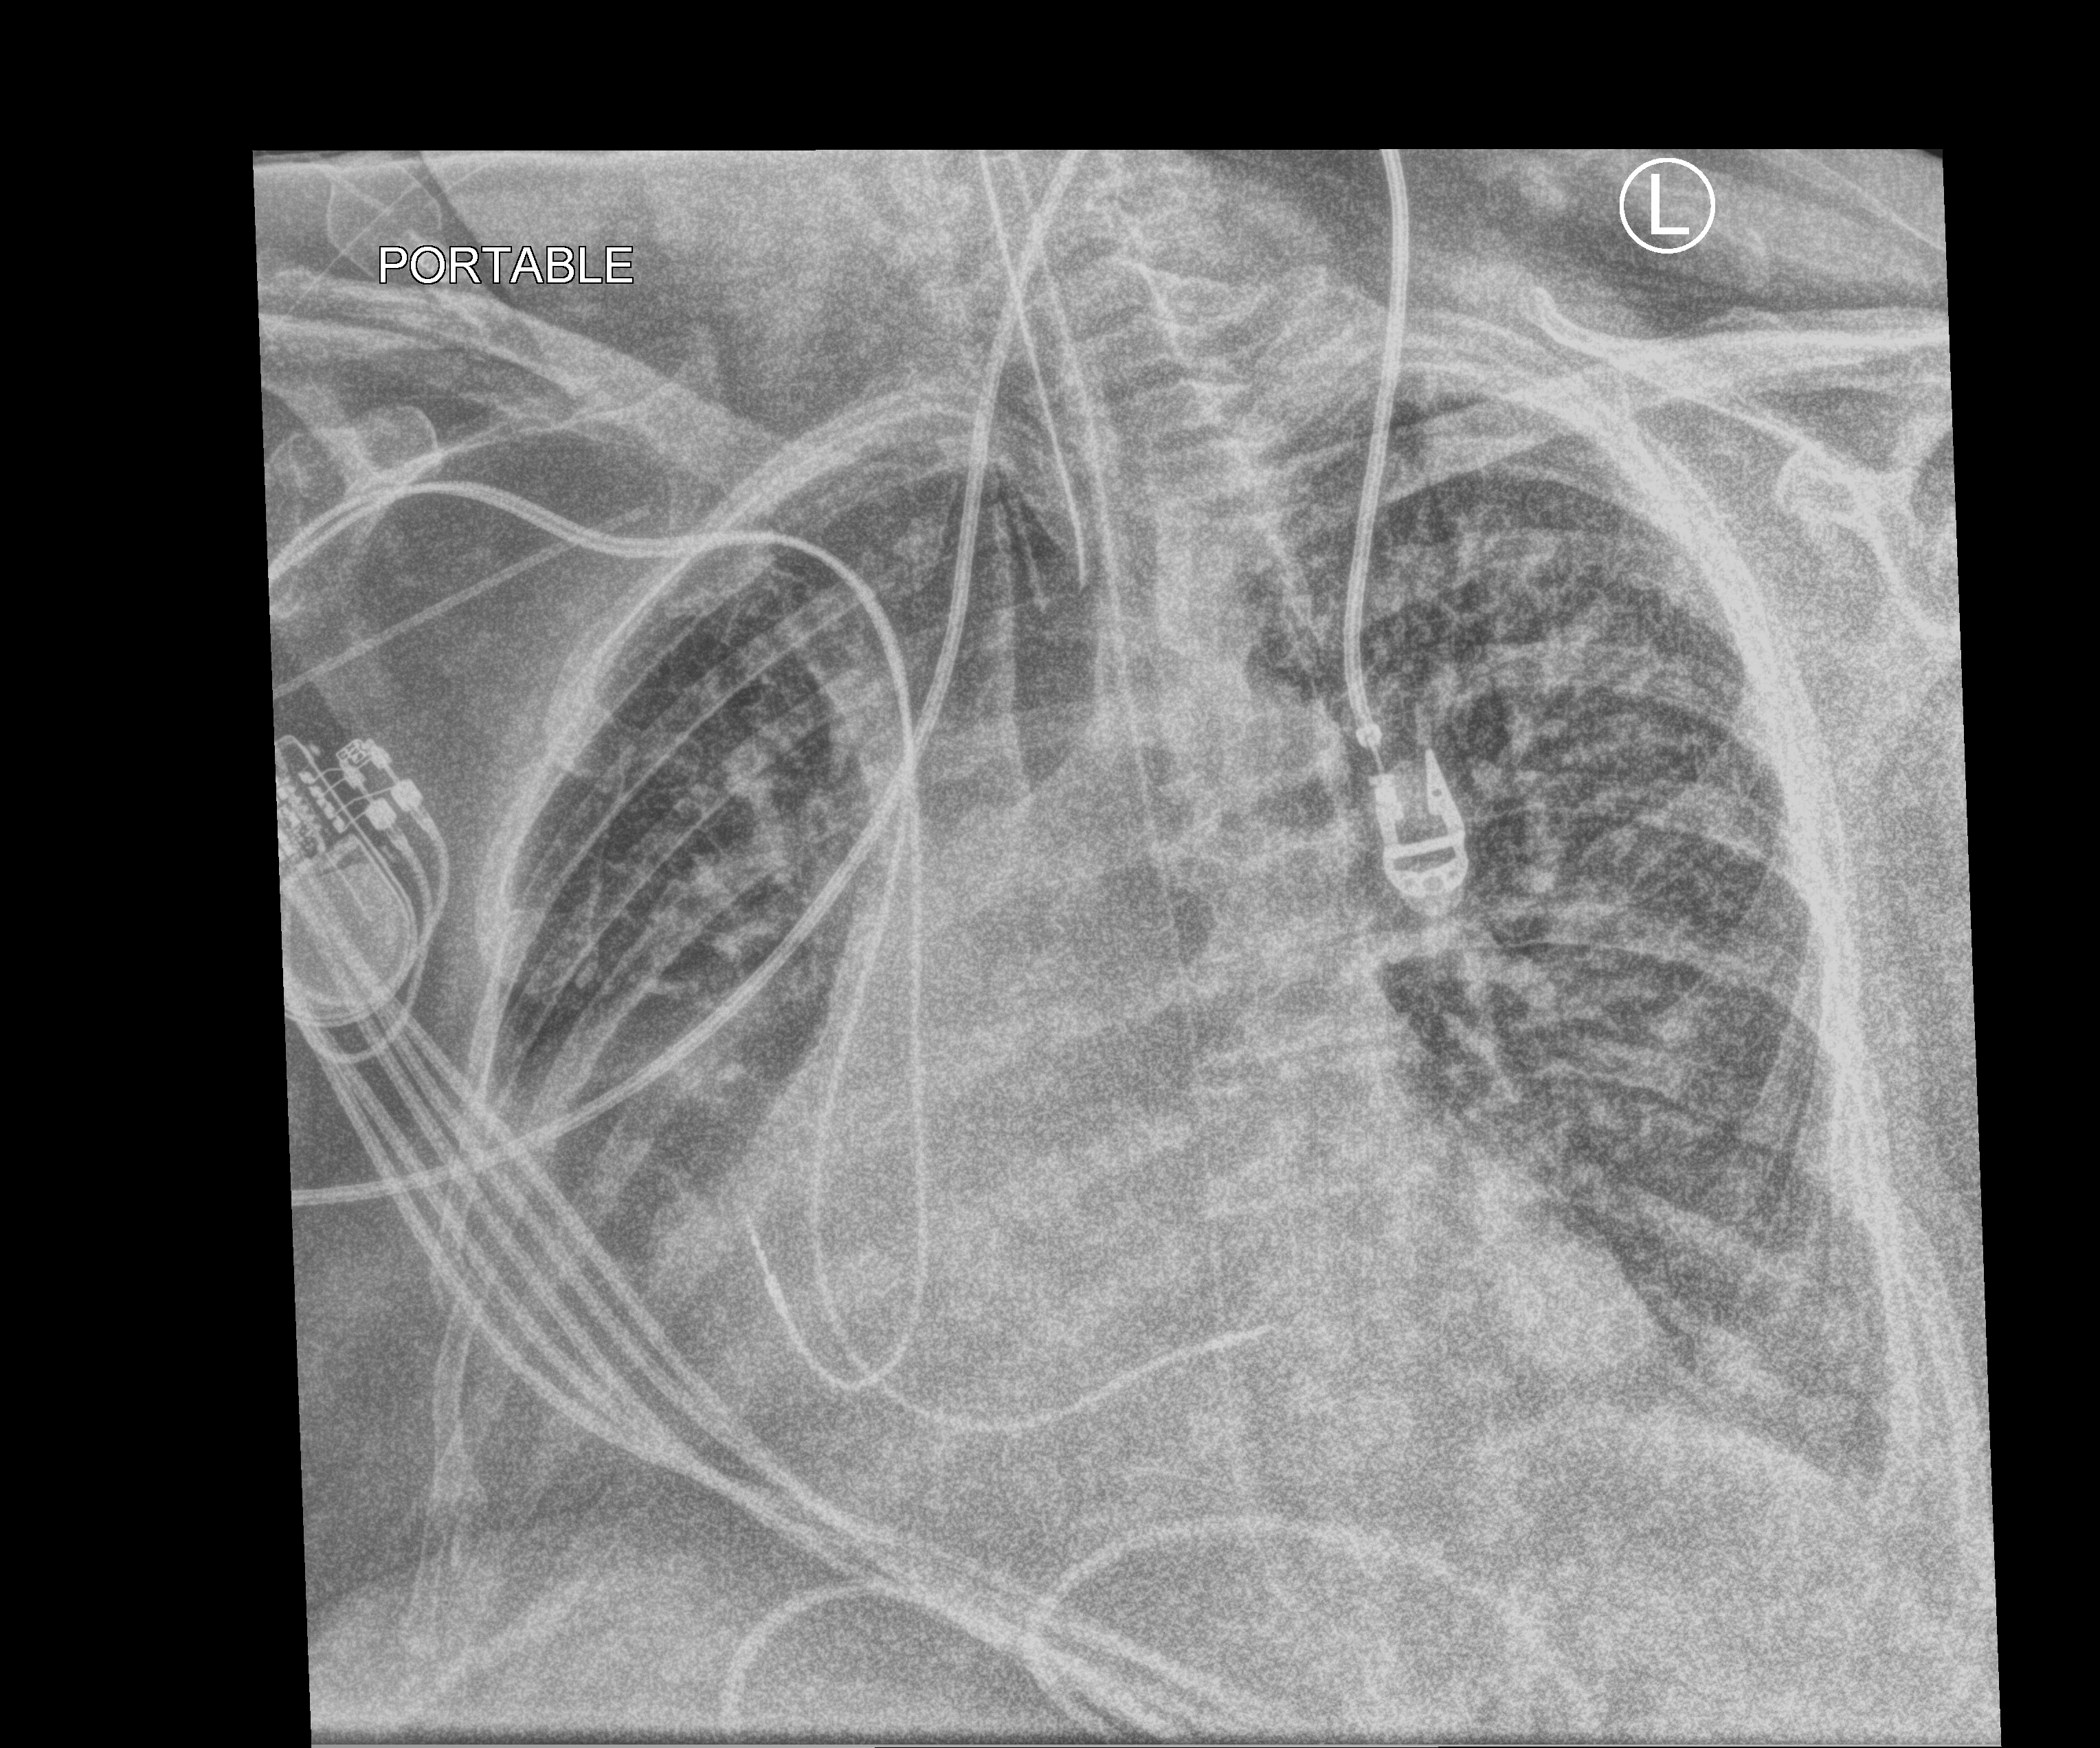
Chest X-ray (portable); anteroposterior (AP) projection. Female patient hospitalised with COVID-19, age 75–90 years.
From the hospital-stay record, not from the radiograph (when in the stay this image was taken is not recorded): other chronic lung disease (admission record): yes.